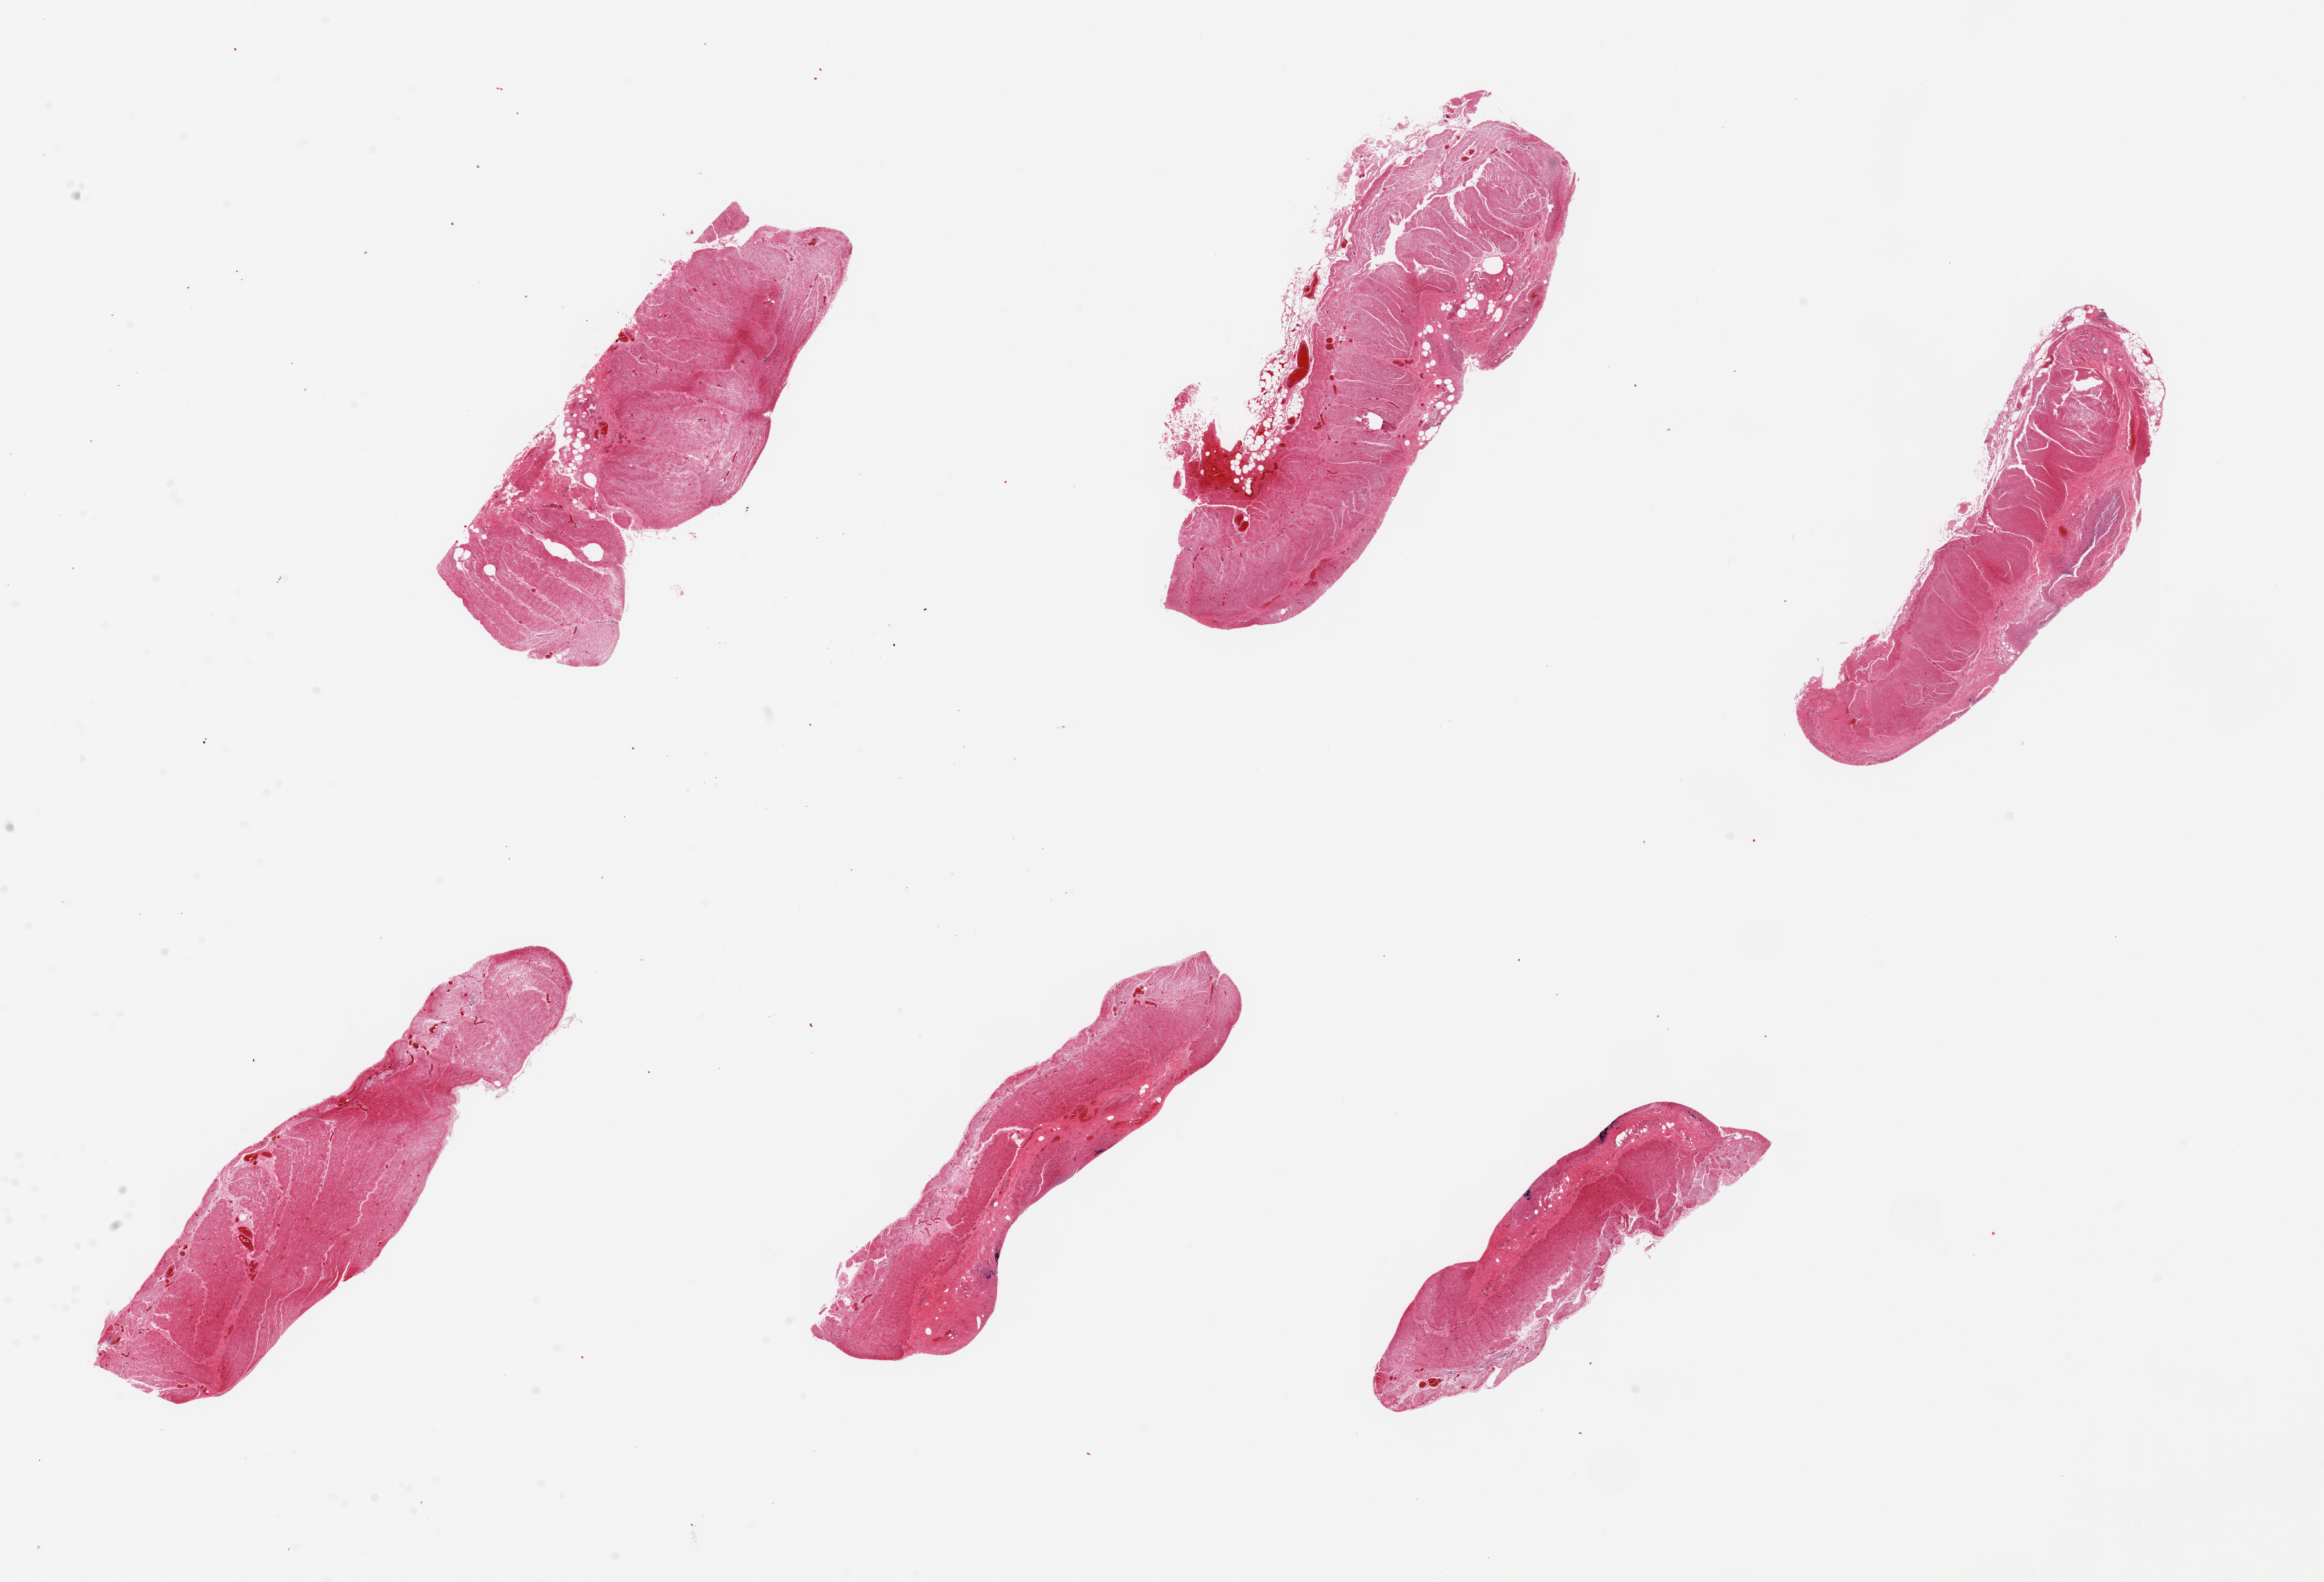
Haematoxylin and eosin whole-slide image — whole scanned area (about 28.5 x 19.4 mm) shown as a low-resolution overview, PAXgene-fixed paraffin-embedded (PFPE) section, section of sigmoid colon (target tissue), tissue donor sample. Donor sex: female.
Pathologist's review note for this sample: 6 pieces, up to 7x3mm; Well dissected without mucosa.